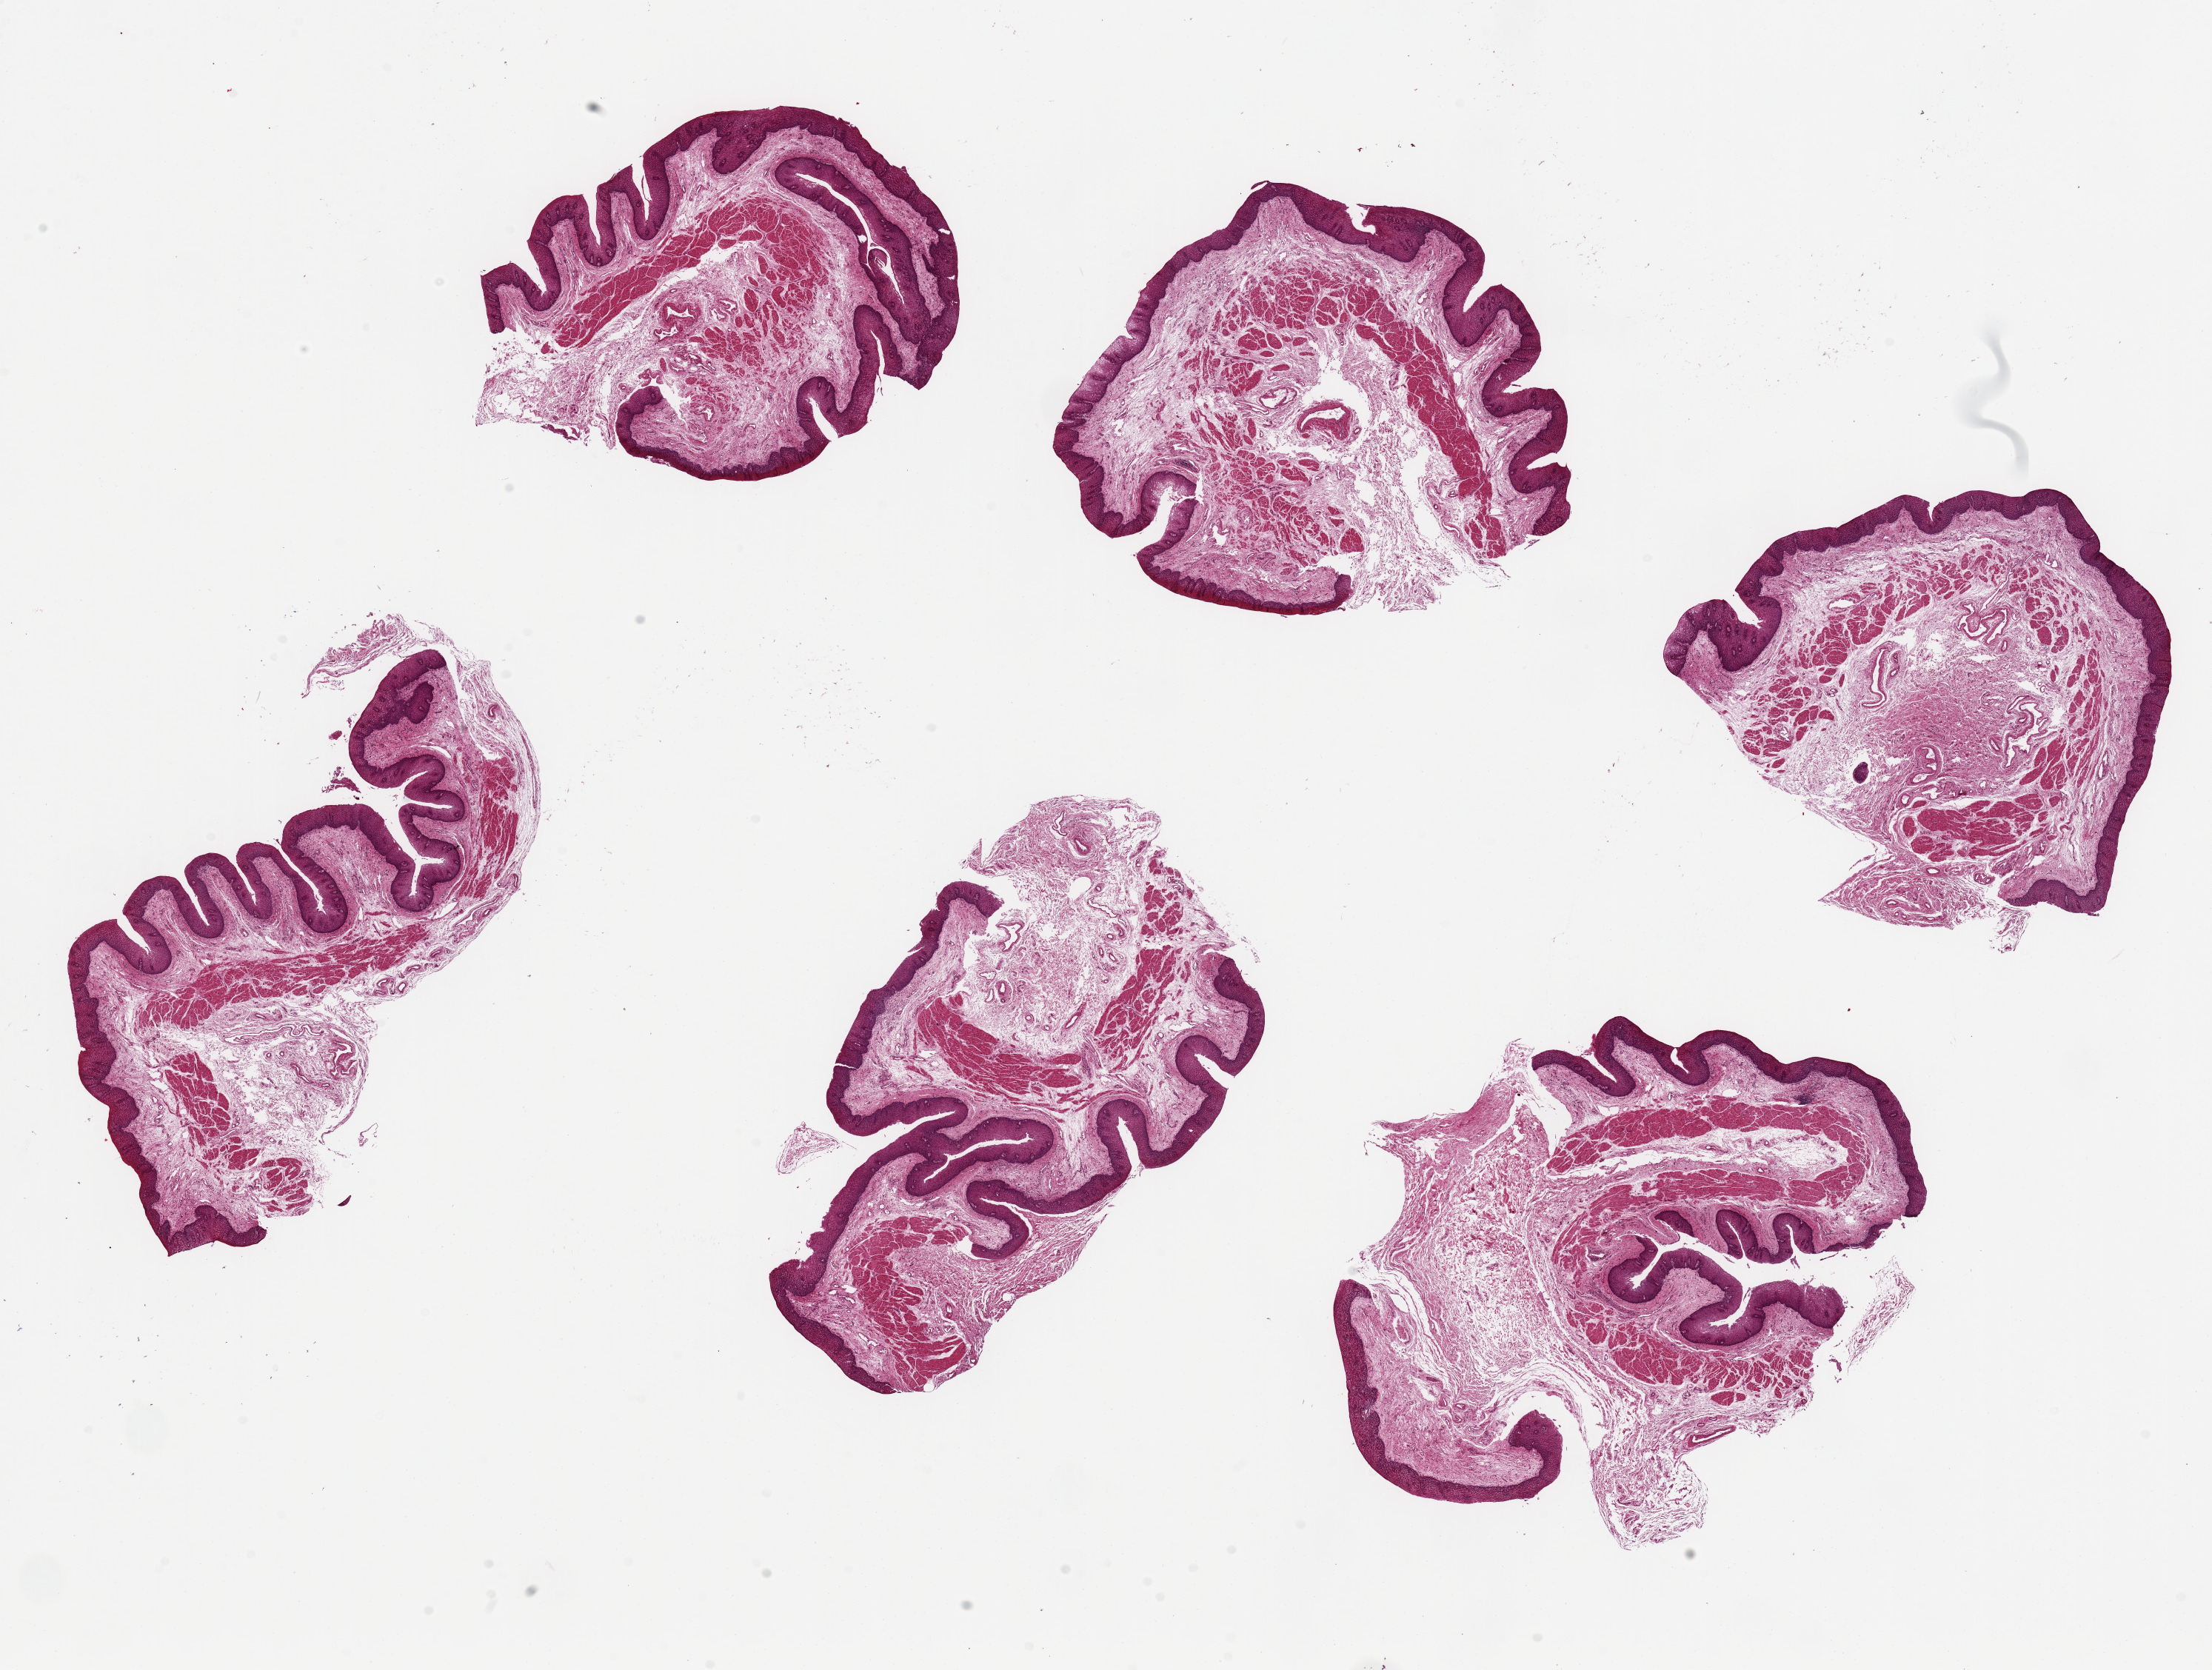
Hematoxylin and eosin (H&E) whole-slide image — shown as a low-resolution overview of the whole scanned area (about 23.6 x 17.8 mm). PAXgene-fixed, paraffin-embedded tissue. Target tissue: esophageal mucous membrane. Tissue donor sample. Female donor.
Review note (as recorded): 6 pieces up to 6x4 mm; lots of good squamous mucosa.